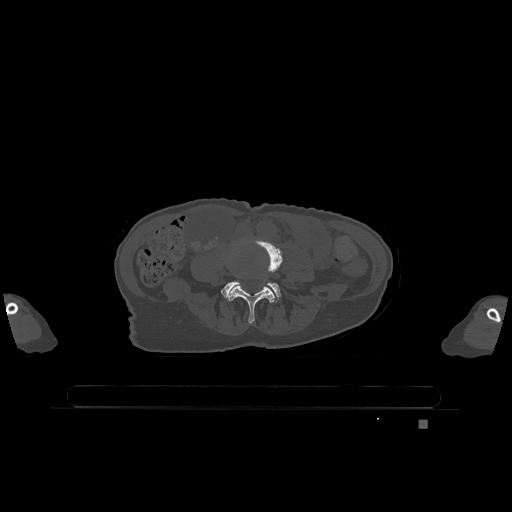
CT including the spine, one axial slice. Bone window (W 1800 / L 400 HU). 0.5 mm slice thickness. 512 × 512 image matrix. Patient: female, 74 years. From the clinical record (not read from this slice): primary cancer: lung.
Structures marked on this image (semi-automatic segmentation, software-assisted and operator-edited):
- L4 vertebra: bounding box (x1, y1, x2, y2) in pixels: (226, 239, 283, 323)
- L5 vertebra: (221, 281, 281, 302)